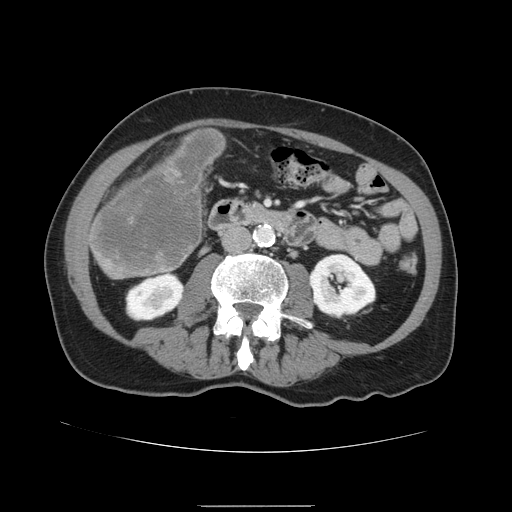
Contrast-enhanced abdominal CT, one axial slice. Position 35 of 168 along the scan axis. Intravenous contrast given. Soft-tissue window (W 400 / L 40 HU). 512 × 512 image matrix, field of view 386 × 386 mm. Male patient, age 74 years. Case-level facts recorded for this patient, not image findings: diagnosis: colorectal cancer liver metastases, imaged before liver resection; multiple liver metastases: no; largest metastasis: 14.5 cm; disease in both lobes: yes.
Outlined on this slice (manually delineated by an expert):
- liver: box from (x=89, y=129) to (x=226, y=280) px
- liver metastasis: (x=93, y=131)–(x=224, y=271)